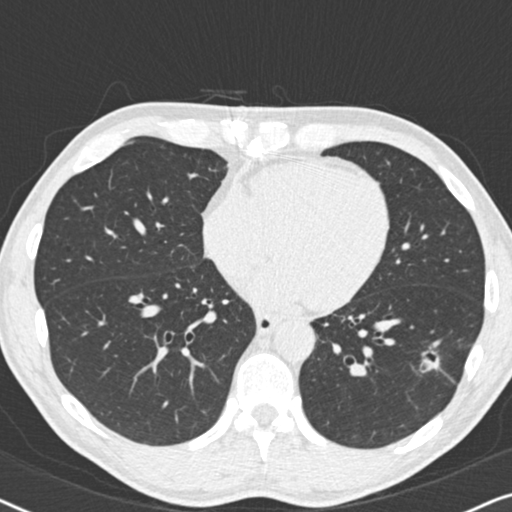
Axial slice from a low-dose chest CT screening exam; second annual screen; lung window (W 1500 / L -600 HU); standard (soft-tissue) reconstruction kernel (B30f). Male participant, aged 59 years at enrolment. Current smoker at enrolment.
Lesion marked by an expert reader, bounding box (x1, y1, x2, y2) in pixels: (412, 337, 461, 382). The screening reader recorded 2 non-calcified nodules or masses ≥4 mm on this exam (left lower lobe, right middle lobe); which of them this box marks is not recorded. Later outcome: lung cancer diagnosed 484 days after this screen — adenocarcinoma, NOS, left lower lobe, poorly differentiated (G3), stage IA (AJCC 6th edition), 20 mm at pathology.